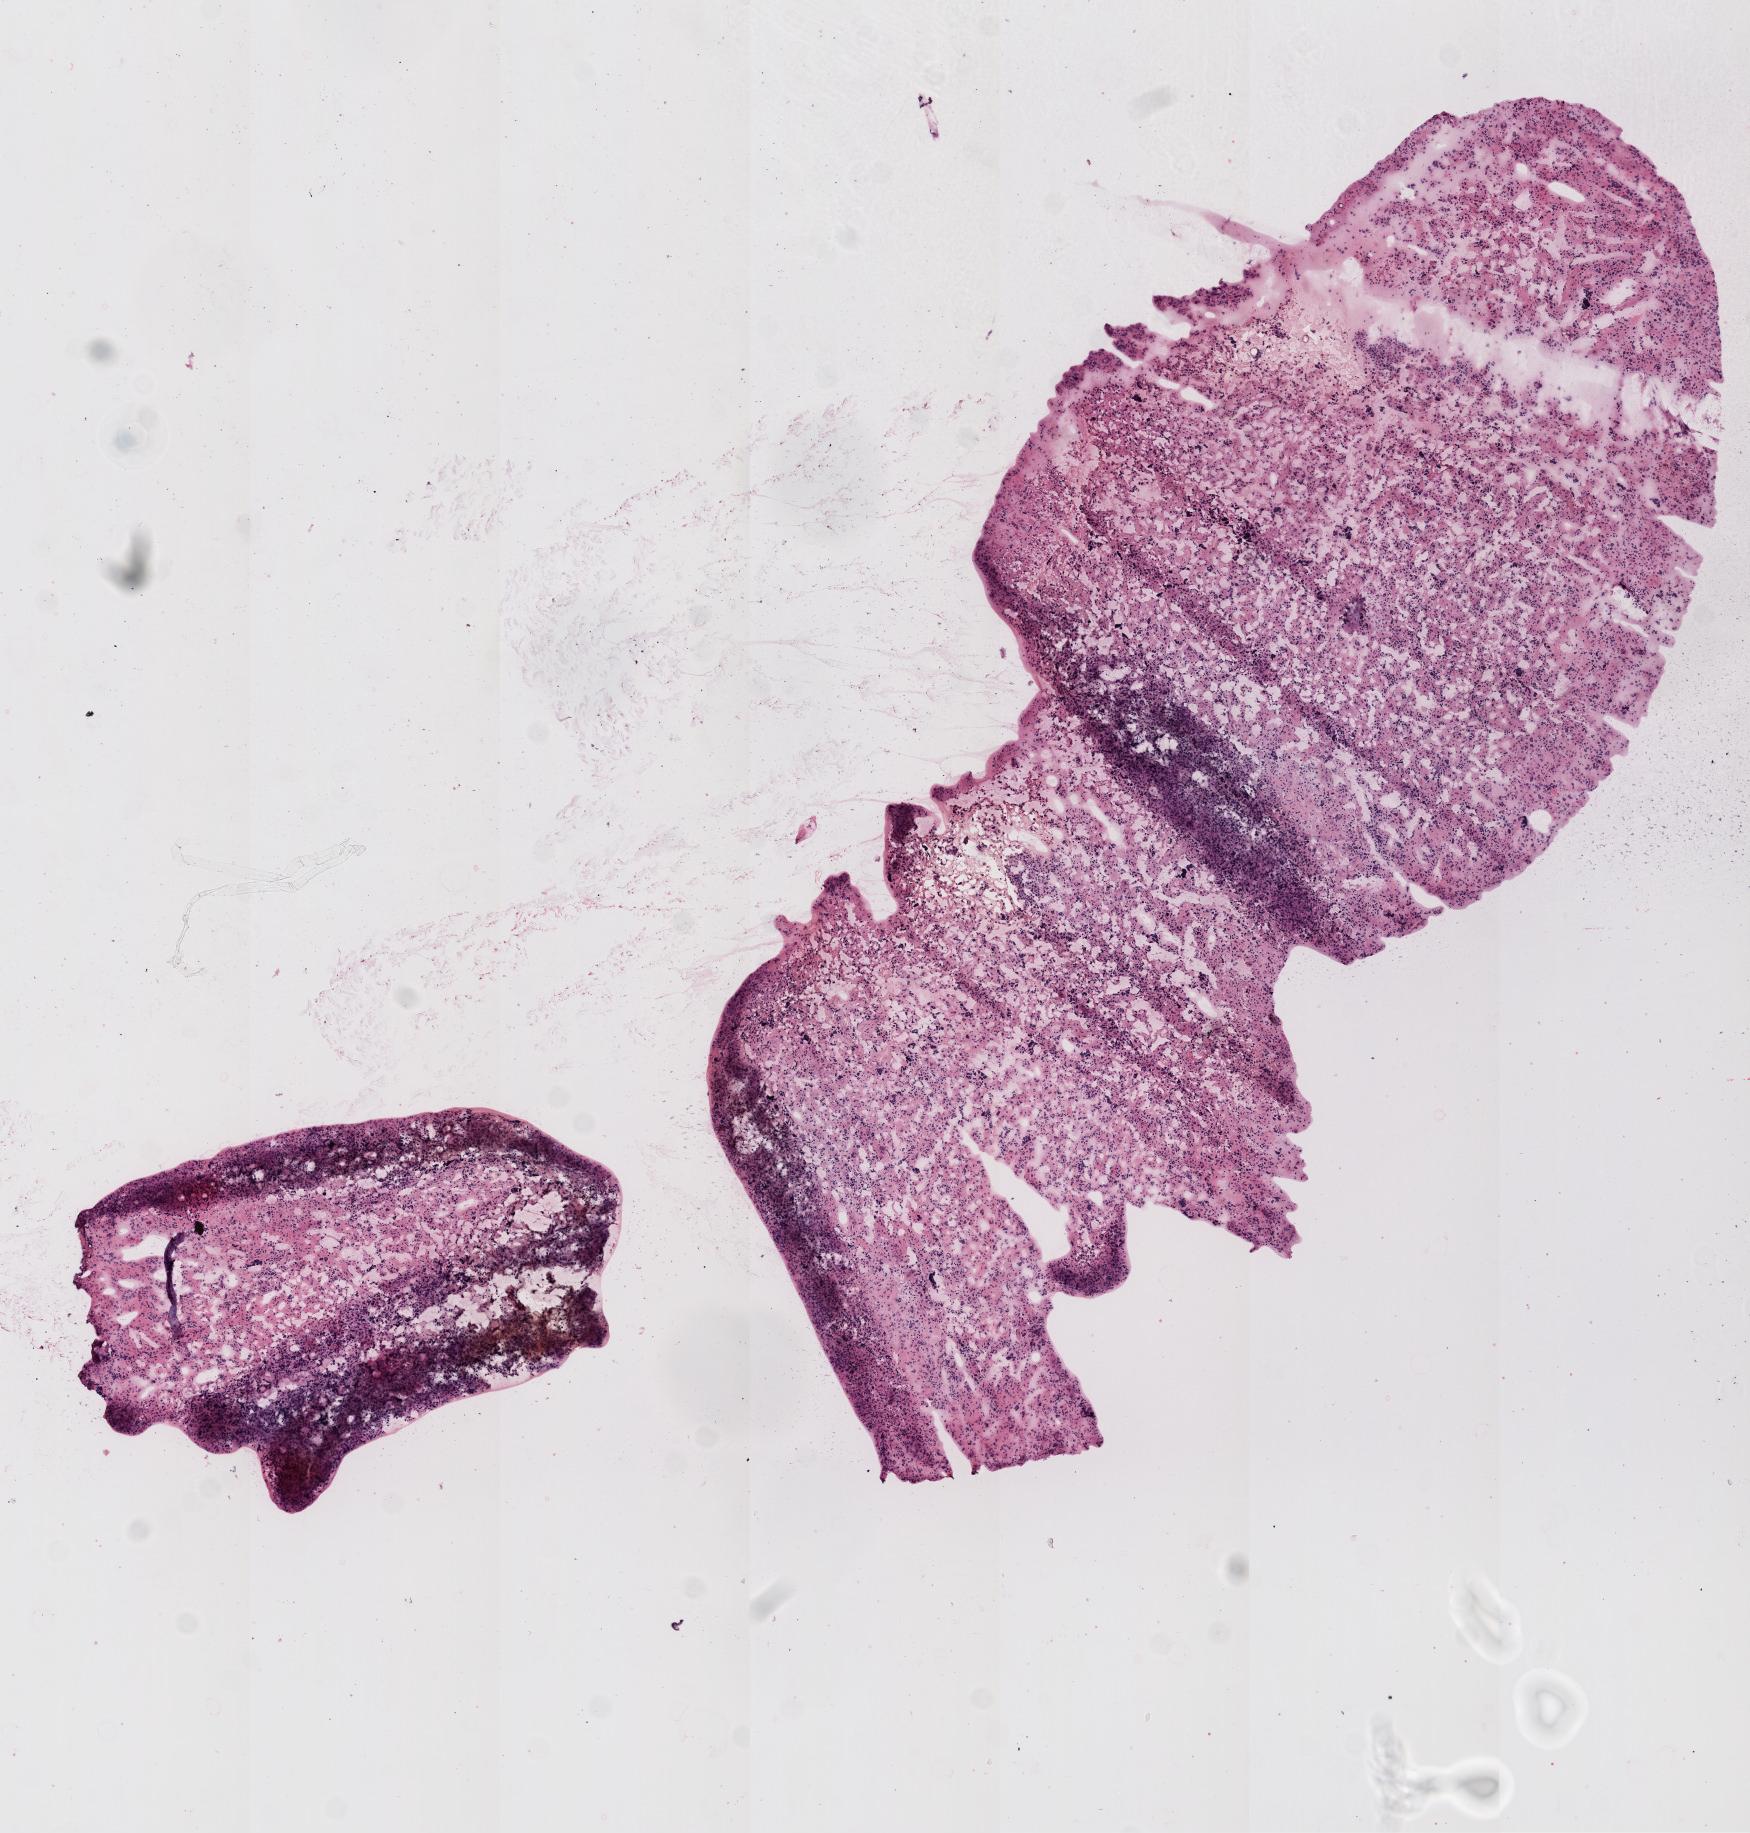
Whole-slide histology image, H&E-stained — a low-resolution overview of the entire scanned area, about 7.0 x 7.4 mm. Frozen section from the top of the tissue portion. Brain, primary tumour sample. Male, age 59 years at initial diagnosis. Composition of this section per pathologist review: tumour cells 100%, tumour nuclei 75%, normal cells 0%, stromal cells 0%, necrosis 0%.
Pathologic diagnosis: Glioblastoma.